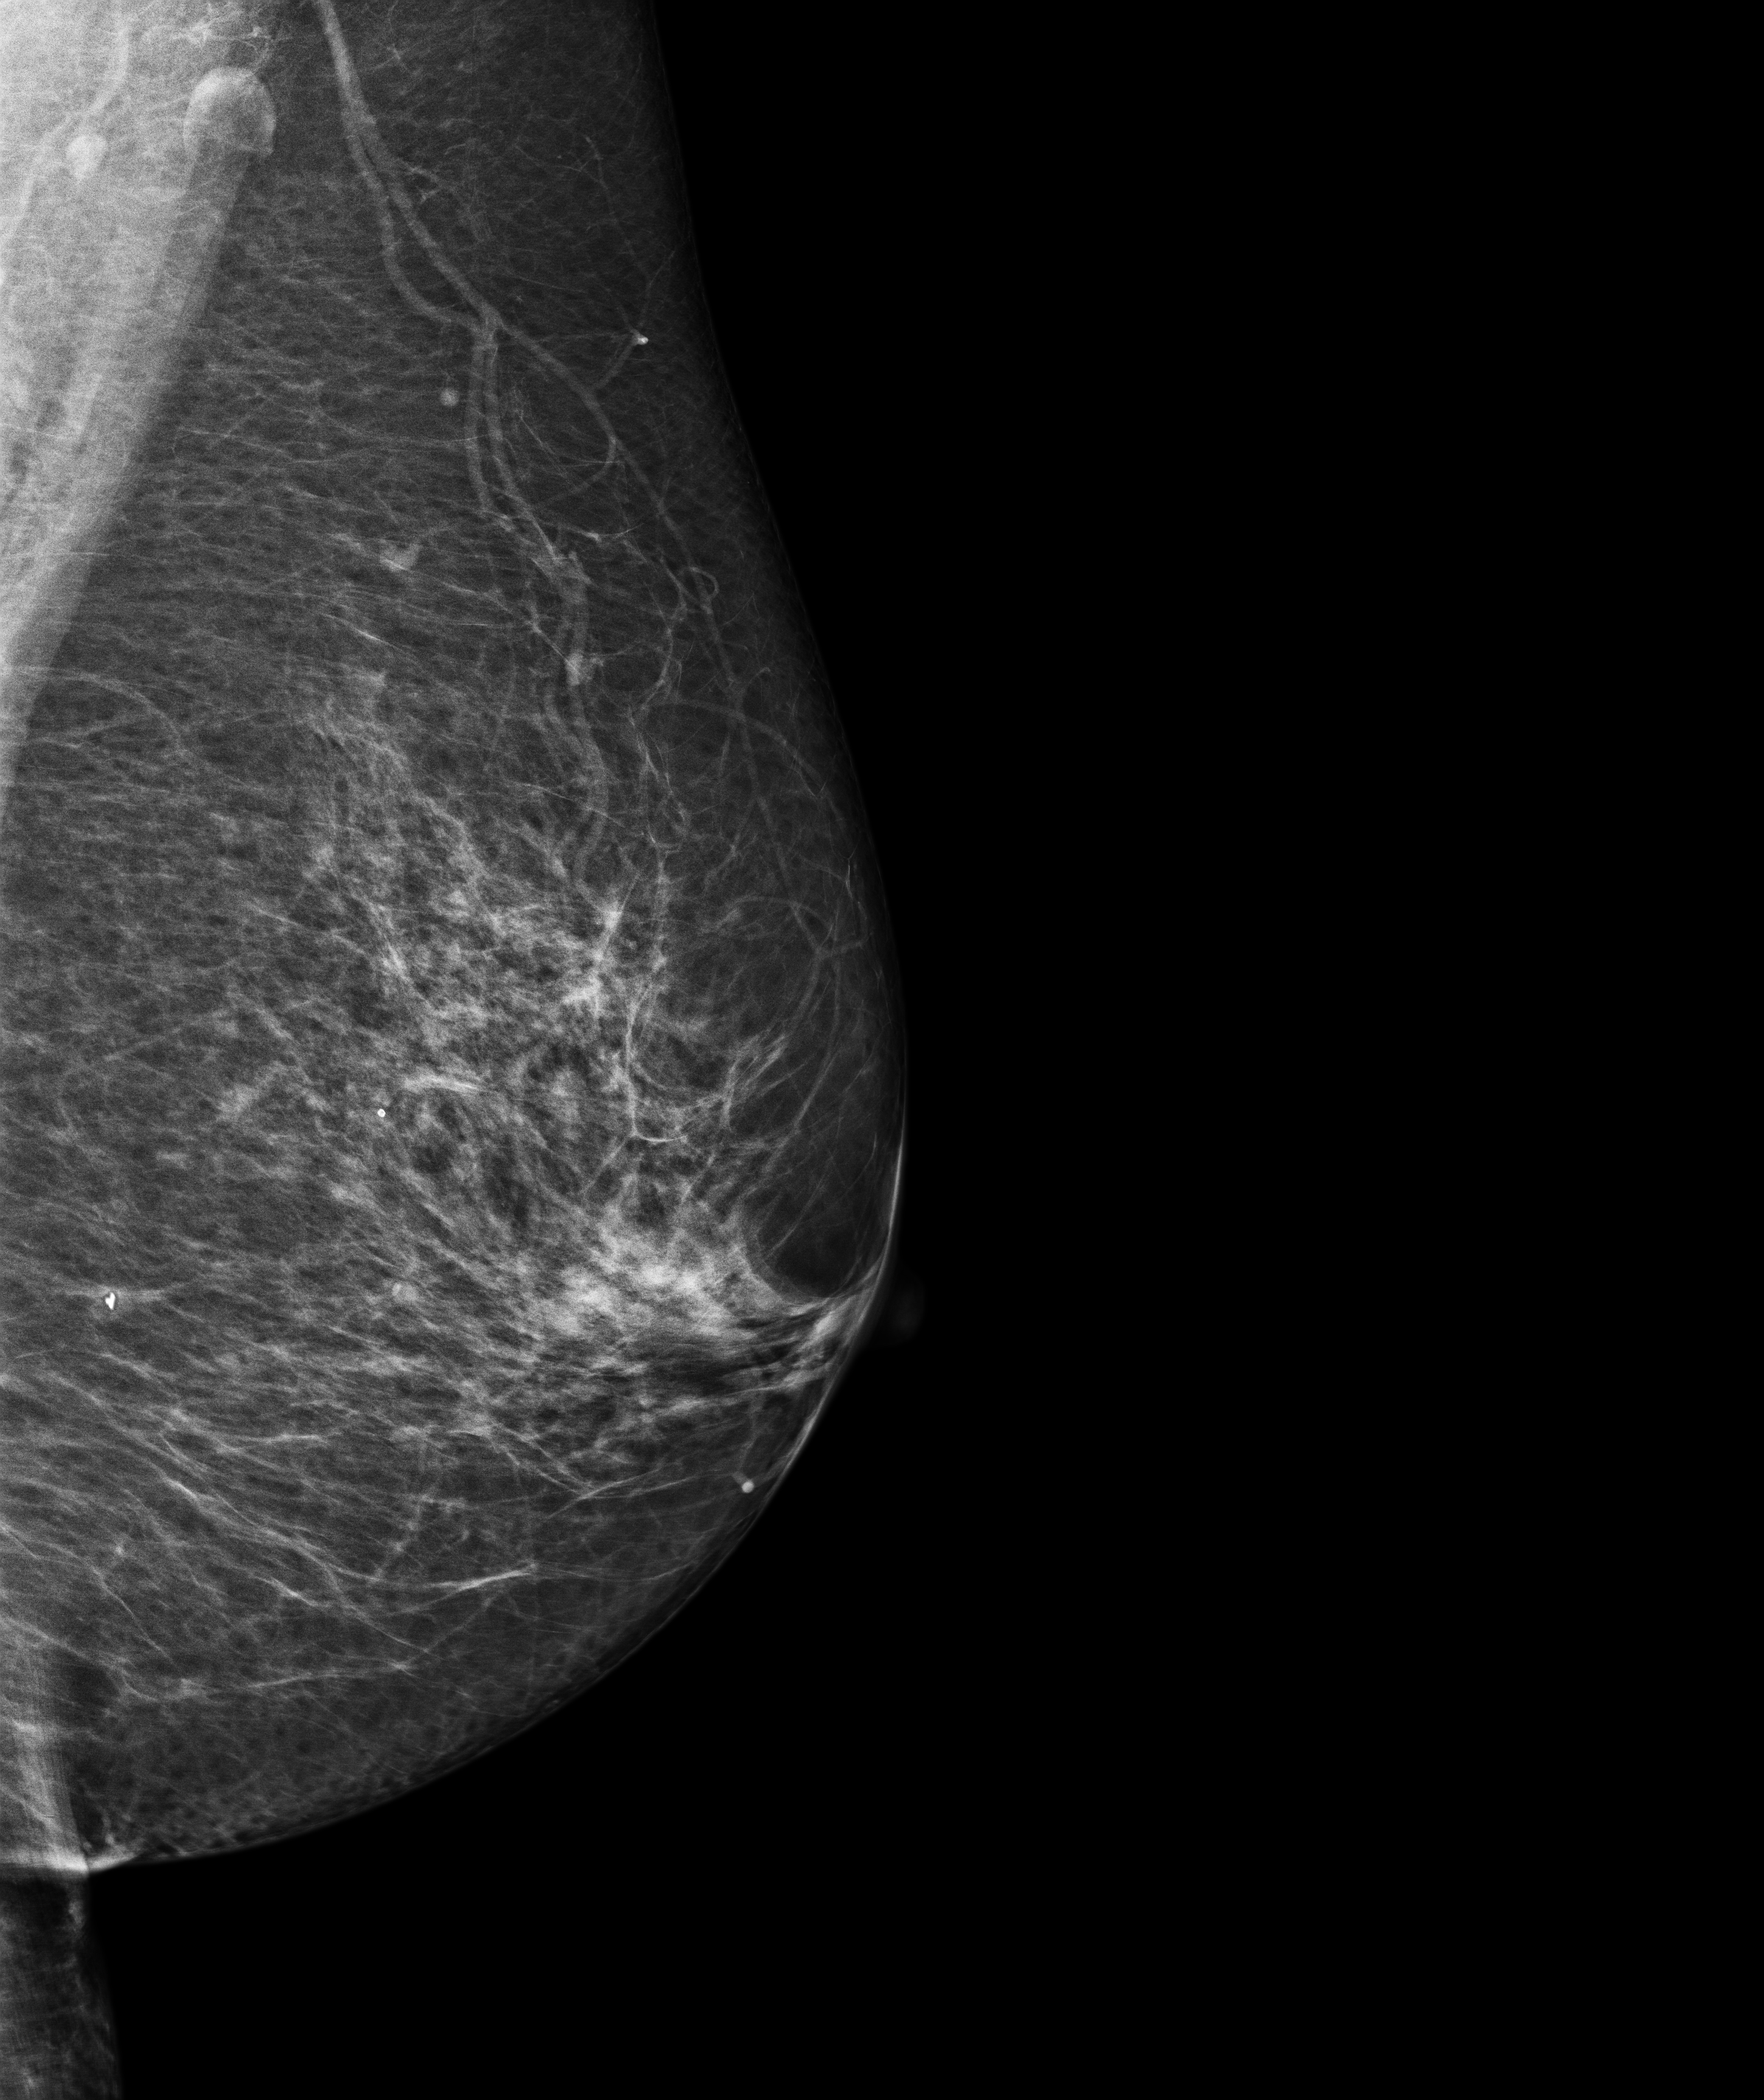
Annual screening mammography examination, system: Senographe Pristina. Female patient, age 54 years.
Image type: full-field digital mammogram. Breast: left. Projection: medio-lateral oblique projection.